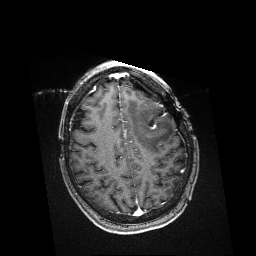
Brain MRI from a brain-tumour surgery series, one axial slice. Position 123 of 176 along the scan axis. T1-weighted post-contrast. 1 mm slice thickness. 256 × 256 image matrix. Case-level facts recorded for this patient, not image findings: histopathology: Metastatic Melanoma; tumour location: Left Frontal.
Annotated regions visible in this slice (expert manual segmentation):
- residual tumour: box from (x=150, y=124) to (x=156, y=129) px